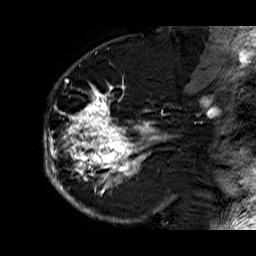
Breast MRI (dynamic contrast-enhanced), one sagittal slice; slice 40 of 60 in the series (ordered by position); dynamic contrast-enhanced series, time point 2 of 6 at this slice position (early post-contrast); 1.5 T; TE 6.3 ms, TR 32.9 ms; 4 mm slice thickness; 256 × 256 image matrix, field of view 200 × 200 mm. Female patient. From the clinical record (not read from this slice): setting: breast cancer imaged before/during neoadjuvant chemotherapy; receptor status: HR-positive, HER2-negative.
Outlined on this slice (semi-automatically segmented with operator editing):
- analysis volume of interest (the breast-tissue region the enhancement analysis was run in; not a lesion): bounding box <44,74,176,210> (left, top, right, bottom; pixels)
- tumour enhancement mask (voxels above the 100 % enhancement threshold inside the analysis volume of interest): <44,74,171,210>